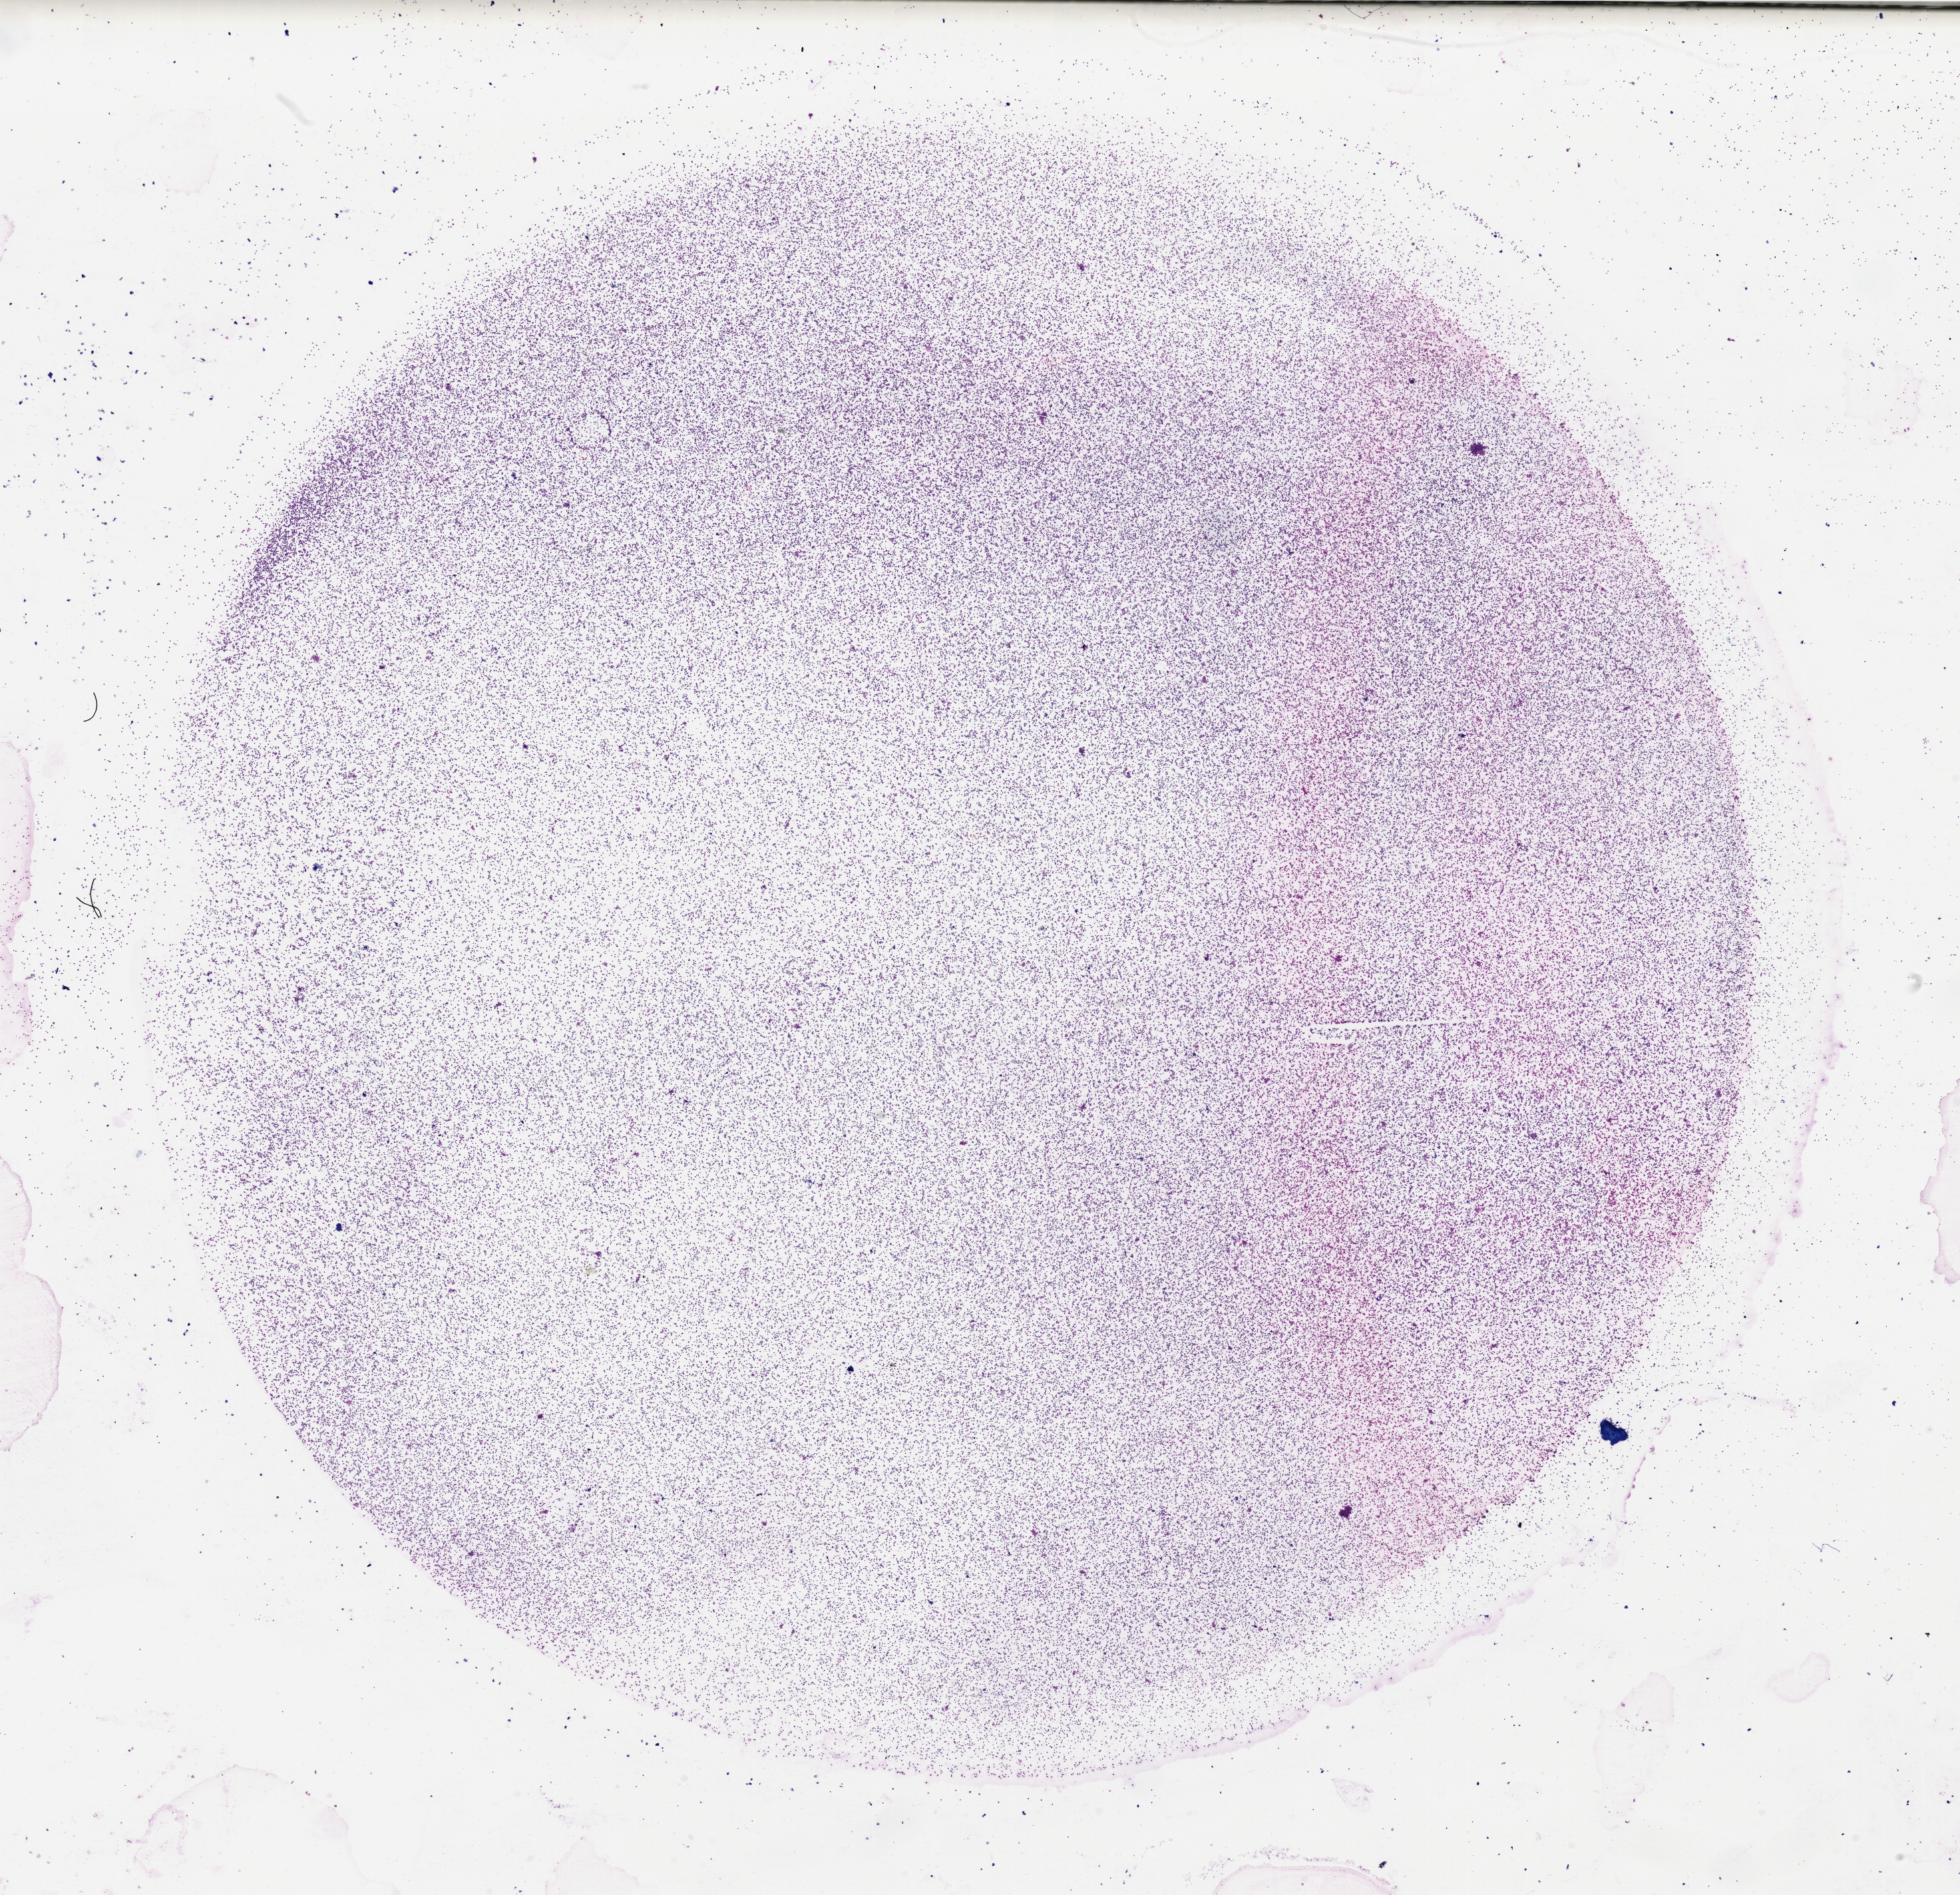
H&E whole-slide image — low-resolution overview of the scanned area, about 23.3 x 22.5 mm (slide scanned at 40x); bone marrow (leukaemic) sample. Male, 45 y/o.
Diagnosis: Acute Myeloid Leukemia.